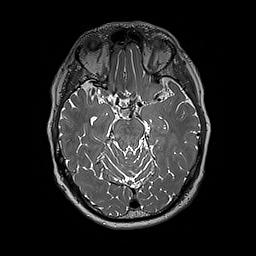
Brain MRI from a brain-tumour surgery series, one axial slice; position 120 of 192 along the scan axis; 256 × 256 image matrix. Case-level facts recorded for this patient, not image findings: histopathology: Glioblastoma; WHO grade: 4; IDH mutation: no.
Outlined on this slice (expert manual segmentation):
- tumour: bounding box (x1, y1, x2, y2) in pixels: (142, 86, 151, 100)